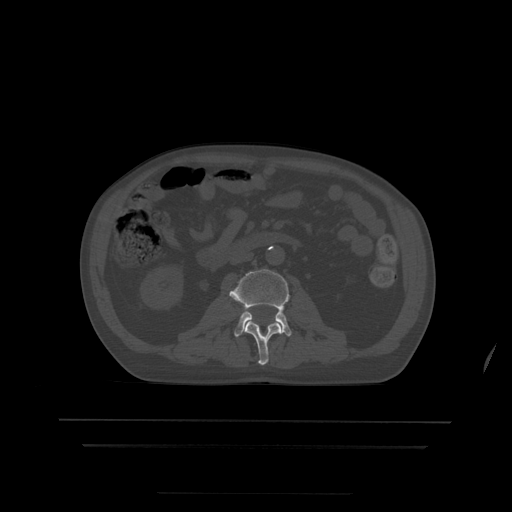
CT including the spine, one axial slice; slice 131 of 522 in the series (ordered by position); bone window (W 1800 / L 400 HU); 1.25 mm slice thickness; 512 × 512 image matrix. Patient age 68 years. From the clinical record (not read from this slice): primary cancer: urothelial.
Annotated regions visible in this slice (semi-automatically segmented with operator editing):
- L2 vertebra: bounding box (x1, y1, x2, y2) in pixels: (245, 321, 282, 366)
- L3 vertebra: (229, 270, 292, 337)